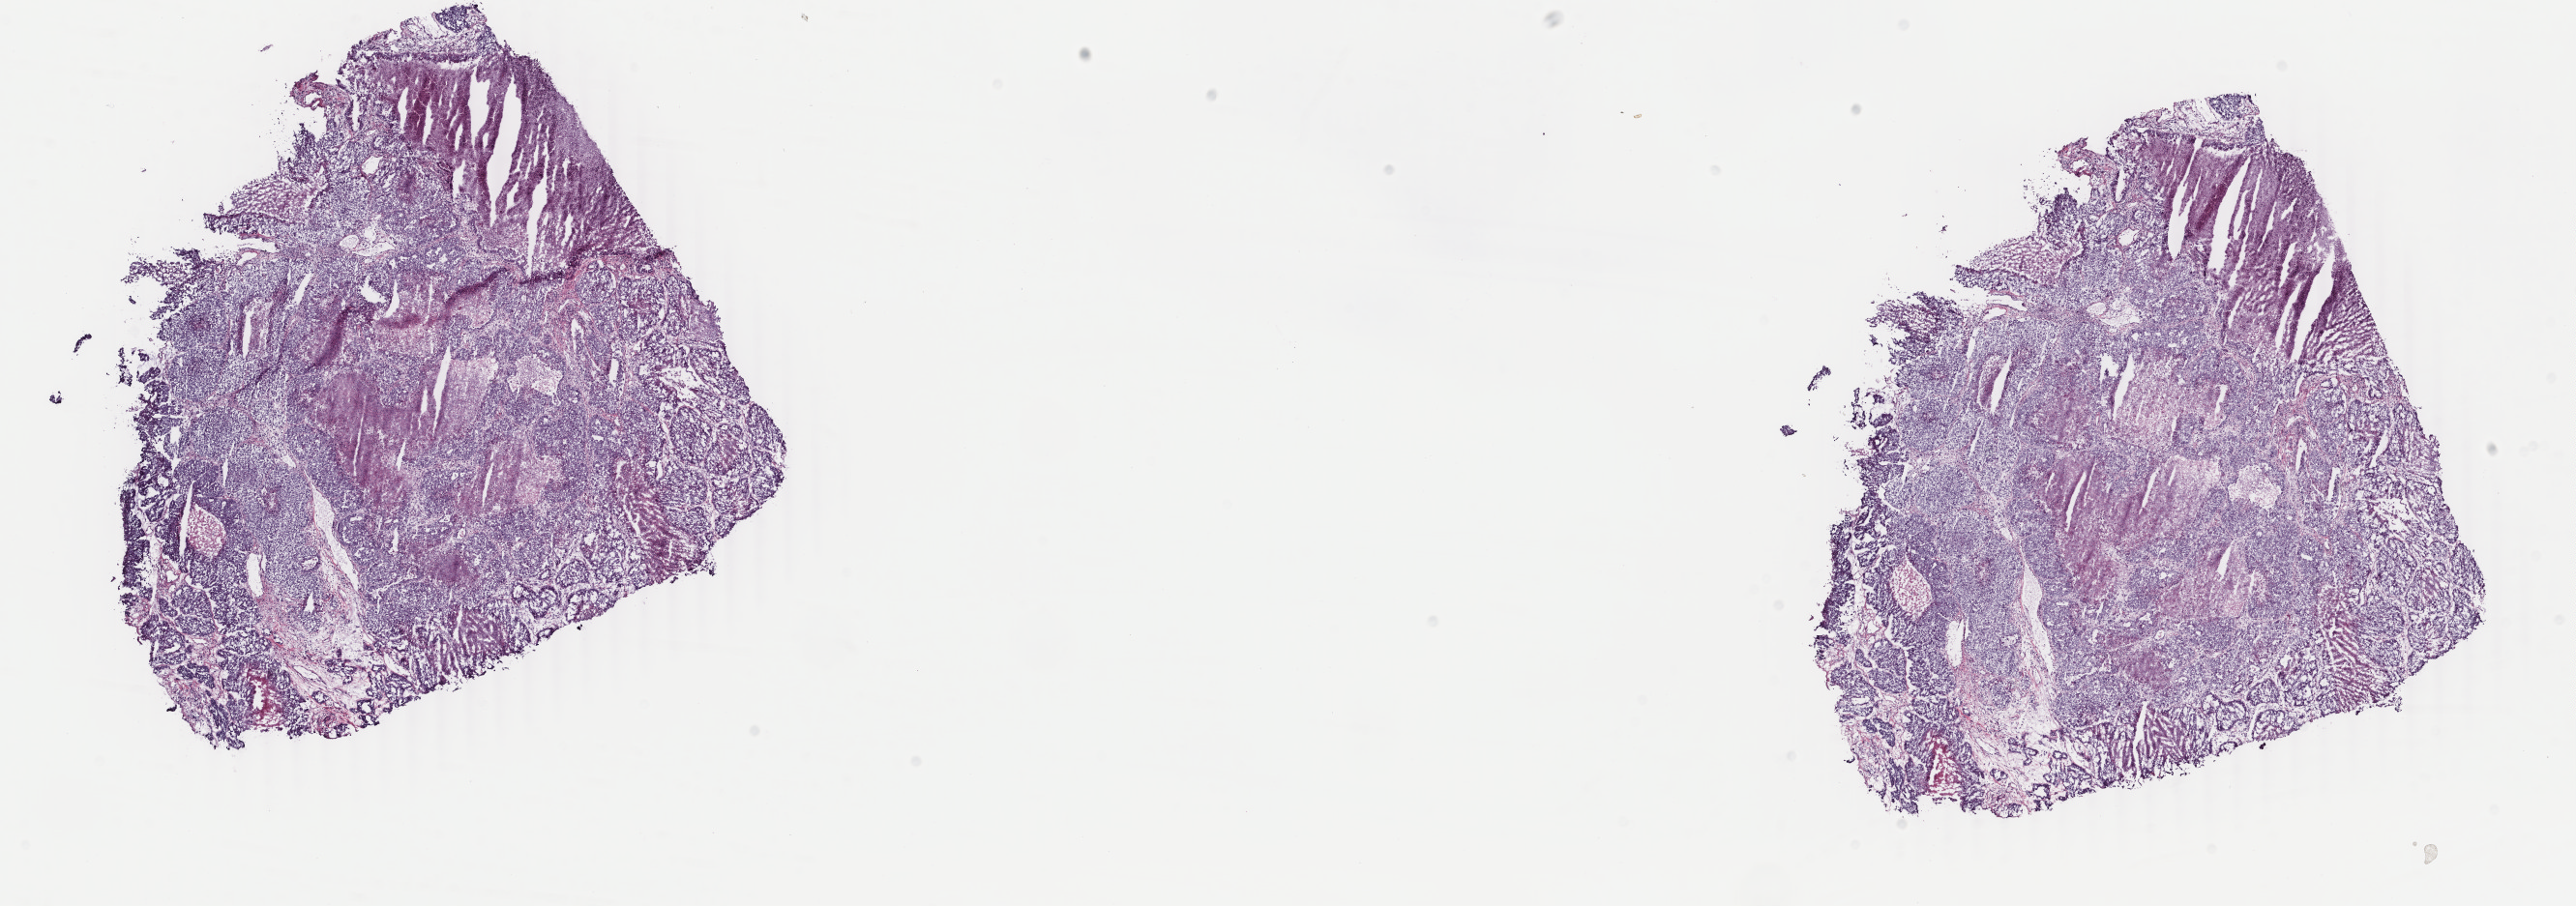
Whole-slide histology image, Hematoxylin and eosin (H&E) stained, a low-resolution overview of the entire scanned area, about 21.2 x 7.5 mm; frozen section from the top of the tissue portion; primary tumour sample from the uterus. Patient: female, age at initial diagnosis 59 years. Pathologist review of this section (percent, as recorded): tumour cells 80%, tumour nuclei 80%, normal cells 0%, stromal cells 20%, necrosis 0%. Infiltration values recorded for this section: lymphocyte infiltration 20%, monocyte infiltration 20%, neutrophil infiltration 40%.
* FIGO stage: IA
* lymph nodes positive (case pathology): 0 of 21 examined
* diagnosis: Carcinosarcoma, NOS